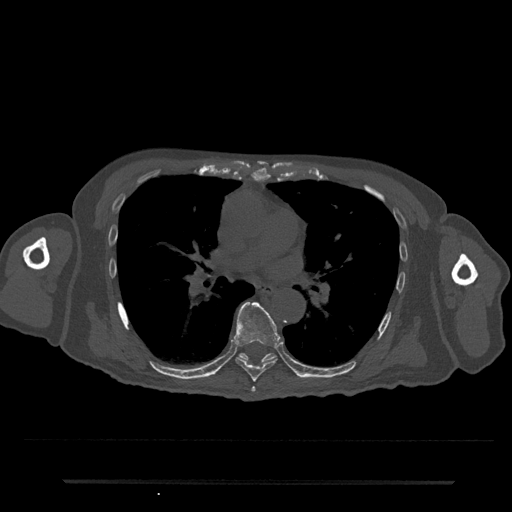
CT including the spine, one axial slice; reconstruction kernel Br40s/3; bone window (W 1800 / L 400 HU); 512 × 512 image matrix. Patient: male, 74 years. From the clinical record (not read from this slice): primary cancer: prostate.
Outlined on this slice (semi-automatically segmented with operator editing):
- T6 vertebra: box from (x=251, y=387) to (x=256, y=392) px
- T7 vertebra: (x=233, y=302)–(x=280, y=382)
- T8 vertebra: (x=238, y=353)–(x=276, y=362)